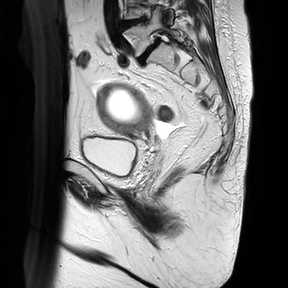
Pelvic MRI for cervical cancer, one sagittal slice; slice 21 of 30 in the series (ordered by position); T2-weighted; 1.5 T; TE 100 ms, TR 4816.3 ms; 4 mm slice thickness; 288 × 288 image matrix, field of view 300 × 300 mm. Female patient, age 74 years.
Annotated regions visible in this slice (manually delineated by an expert):
- uterus and cervix: bounding box [x1, y1, x2, y2] px = [96, 81, 154, 136]